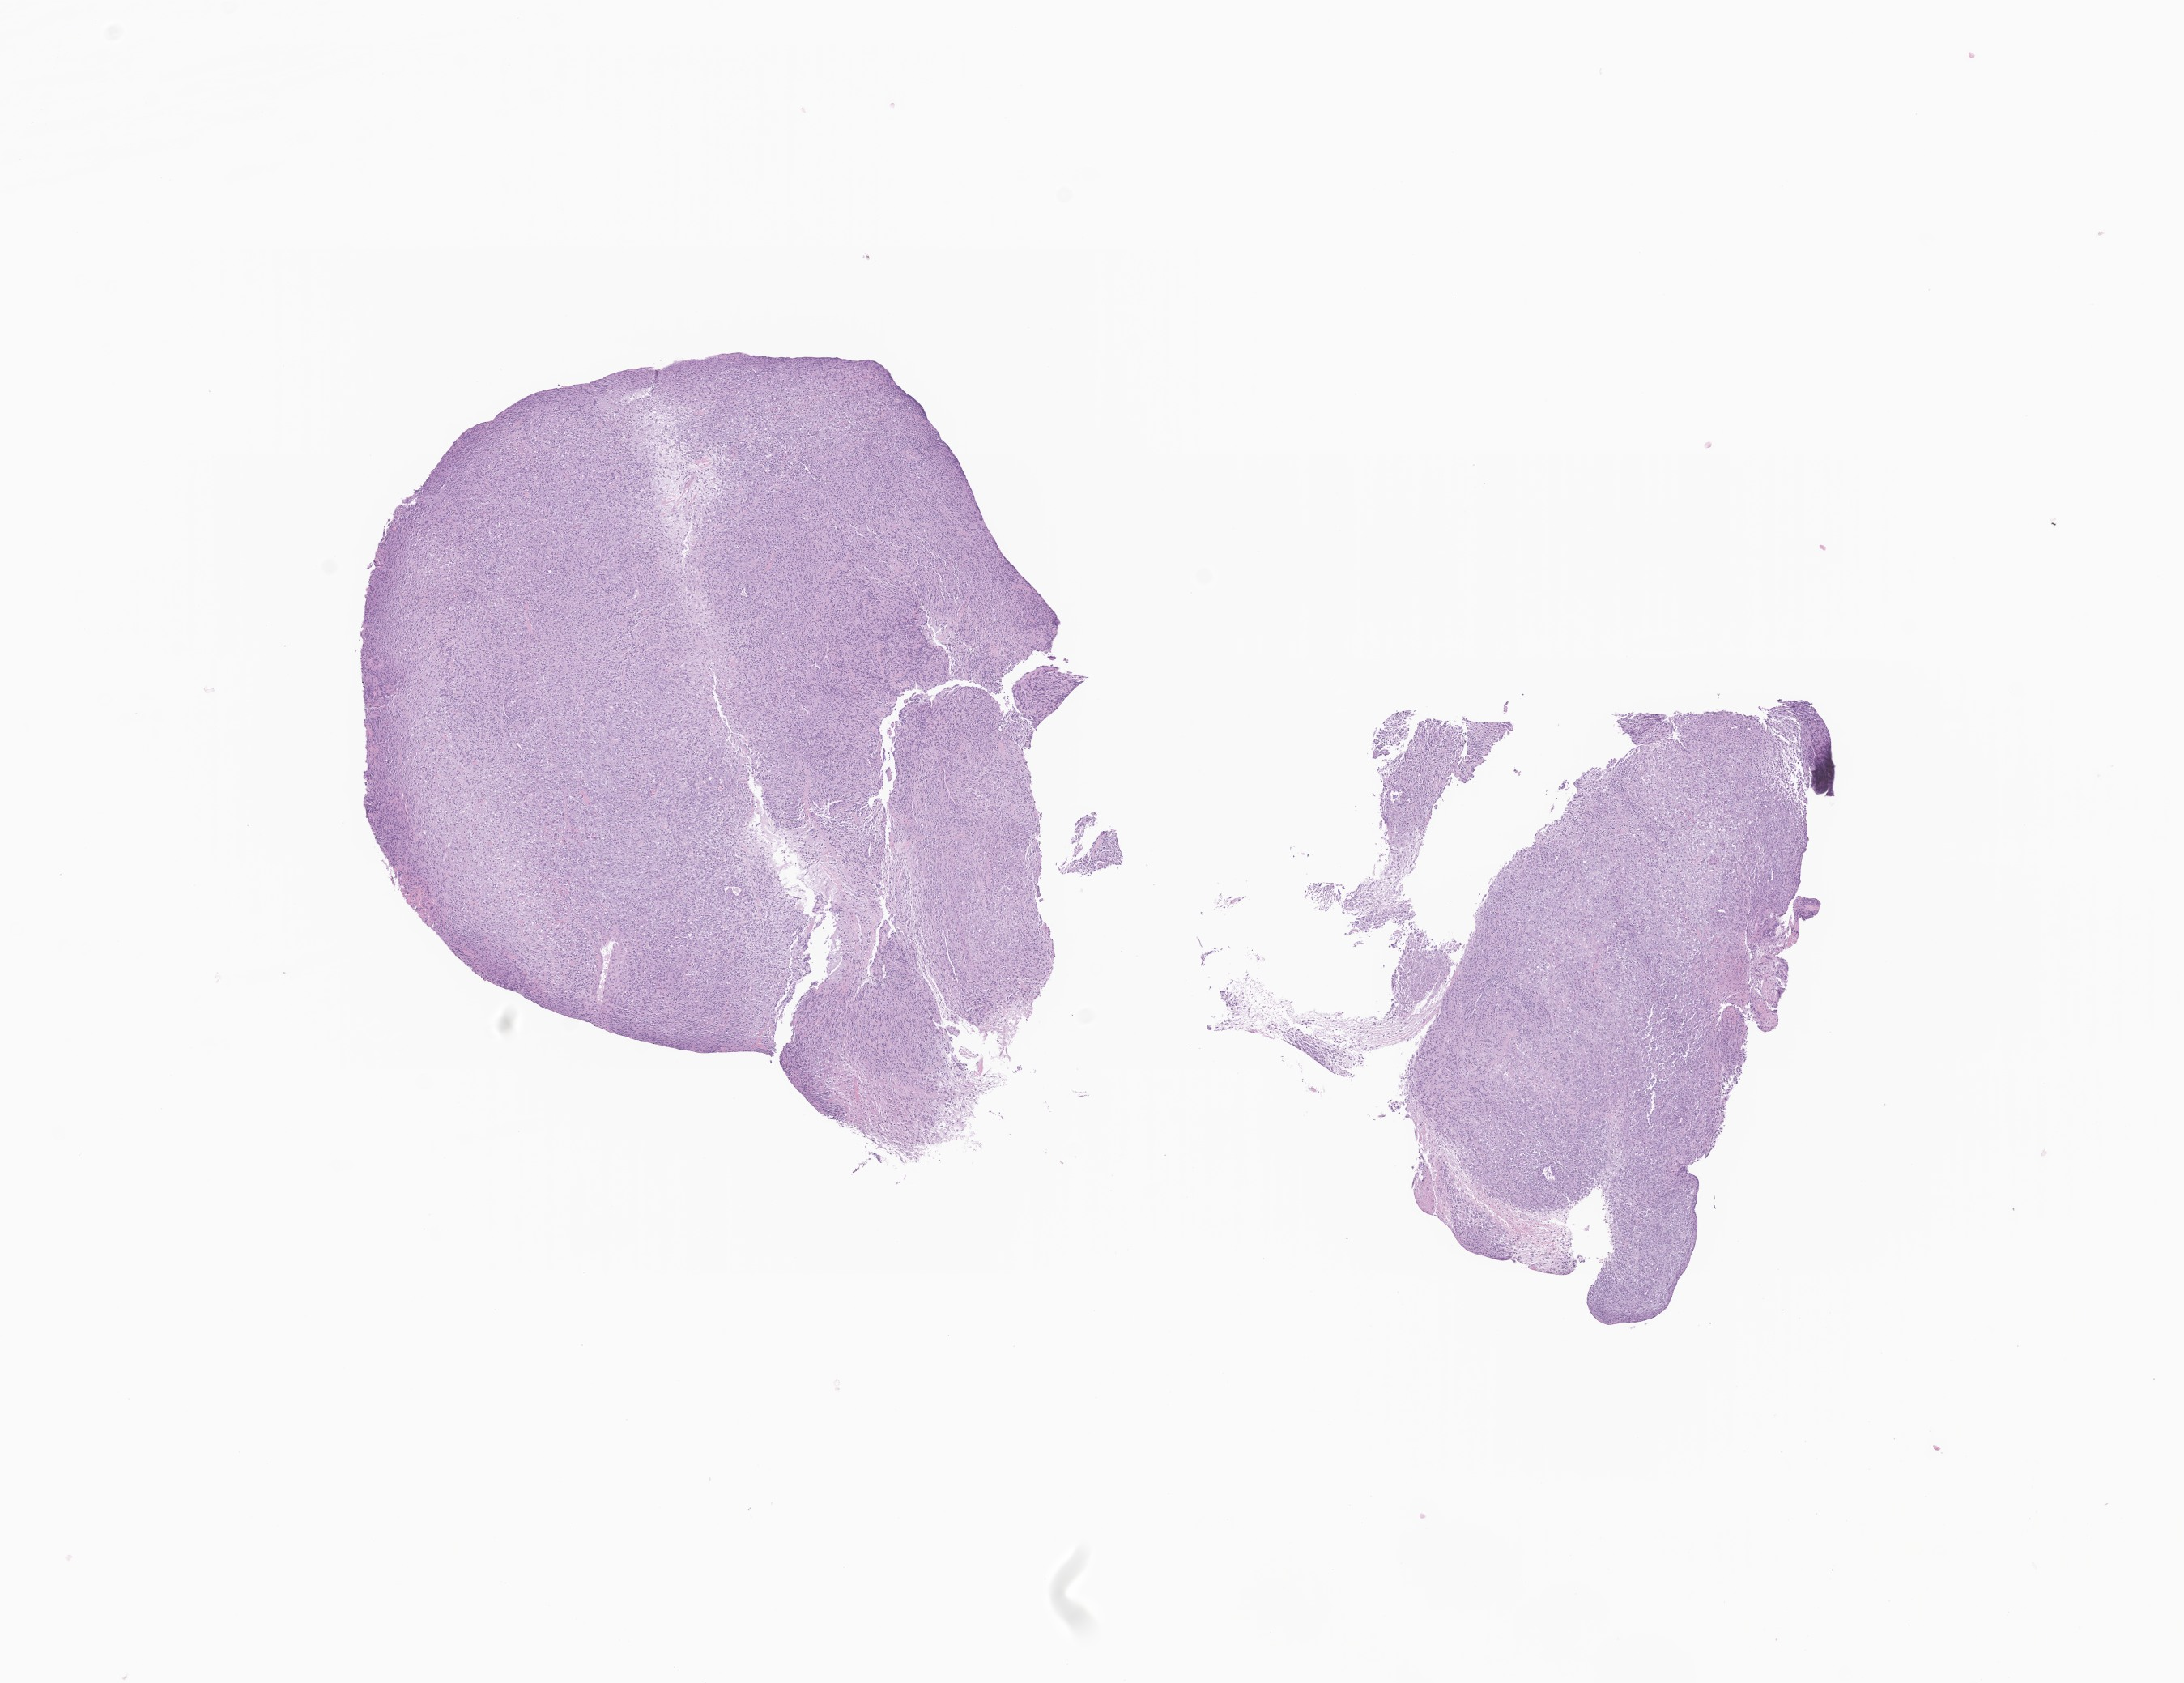
Digitized H&E-stained section of tumor tissue from the soft tissues of head and neck, a low-resolution overview of the entire scanned area, about 11.4 x 8.8 mm. Male patient, age 71 days.
Specimen: formalin-fixed paraffin-embedded section.